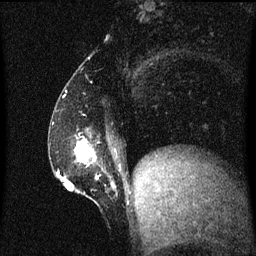
Breast MRI (dynamic contrast-enhanced), one sagittal slice; position 20 of 60 along the scan axis; dynamic contrast-enhanced series, image 2 of 3 at this slice position (ordered by acquisition); 1.5 T; TE 4.2 ms, TR 8.4 ms; 2 mm slice thickness; 256 × 256 image matrix, field of view 200 × 200 mm. Female patient, age 52 years. From the clinical record (not read from this slice): setting: breast cancer imaged before/during neoadjuvant chemotherapy; receptor status: HER2-positive.
Outlined on this slice (semi-automatically segmented with operator editing):
- analysis volume of interest (the breast-tissue region the enhancement analysis was run in; not a lesion): bounding box <62,132,115,203> (left, top, right, bottom; pixels)
- tumour enhancement mask (voxels above the 70 % enhancement threshold inside the analysis volume of interest): <66,140,115,187>